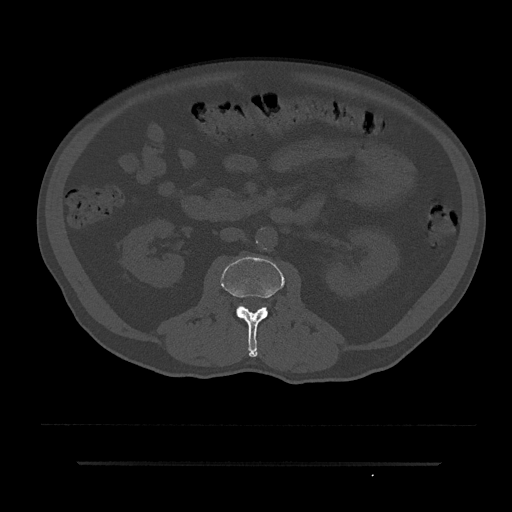
CT including the spine, one axial slice. Position 57 of 797 along the scan axis. Bone window (W 1800 / L 400 HU). 512 × 512 image matrix, field of view 464 × 464 mm. Male patient, age 59 years. Case-level facts recorded for this patient, not image findings: primary cancer: bile ducts.
Outlined on this slice (semi-automatically segmented with operator editing):
- L2 vertebra: box from (x=221, y=256) to (x=285, y=357) px